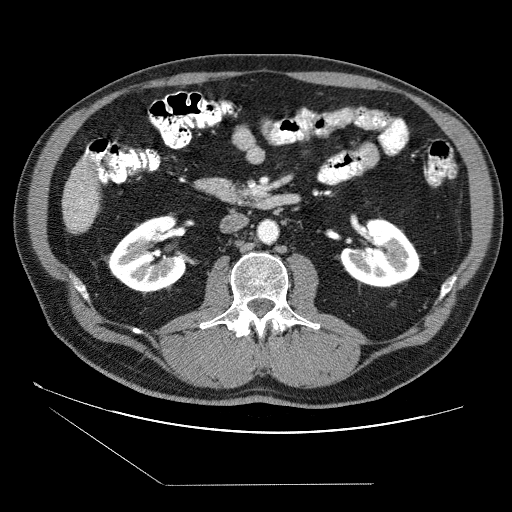
Contrast-enhanced abdominal CT (liver protocol), one axial slice; slice 9 of 87 in the series (ordered by position); soft-tissue window (W 400 / L 40 HU); 2.5 mm slice thickness; 512 × 512 image matrix, field of view 400 × 400 mm. From the clinical record (not read from this slice): diagnosis: hepatocellular carcinoma (patient treated with transarterial chemoembolisation; whether this scan precedes or follows treatment is not stated here); TNM stage (as recorded): Stage-II; Child-Pugh class: B.
Structures marked on this image (semi-automatically segmented with operator editing):
- liver parenchyma outside the tumour (the mass and vessels are separate outlines, so this box may not span the whole liver): bounding box (x1, y1, x2, y2) in pixels: (62, 156, 100, 232)
- liver vessels: (74, 186, 88, 227)